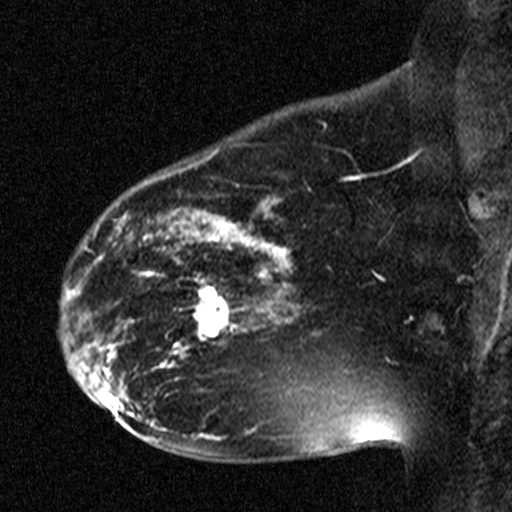
Breast MRI (dynamic contrast-enhanced), one sagittal slice; position 31 of 44 along the scan axis; dynamic contrast-enhanced study with each time point stored as its own series, time point 2 of 3 at this slice position (early post-contrast, ordered by acquisition time); 1.5 T; TE 4.5 ms, TR 11 ms; 512 × 512 image matrix. Patient: female, 38 years. From the clinical record (not read from this slice): setting: breast cancer imaged before/during neoadjuvant chemotherapy; receptor status: HR-positive, HER2-negative.
Annotated regions visible in this slice (semi-automatically segmented with operator editing):
- analysis volume of interest (the breast-tissue region the enhancement analysis was run in; not a lesion): bounding box (x1, y1, x2, y2) in pixels: (176, 272, 251, 349)
- tumour enhancement mask (voxels above the 90 % enhancement threshold inside the analysis volume of interest): (176, 276, 251, 347)